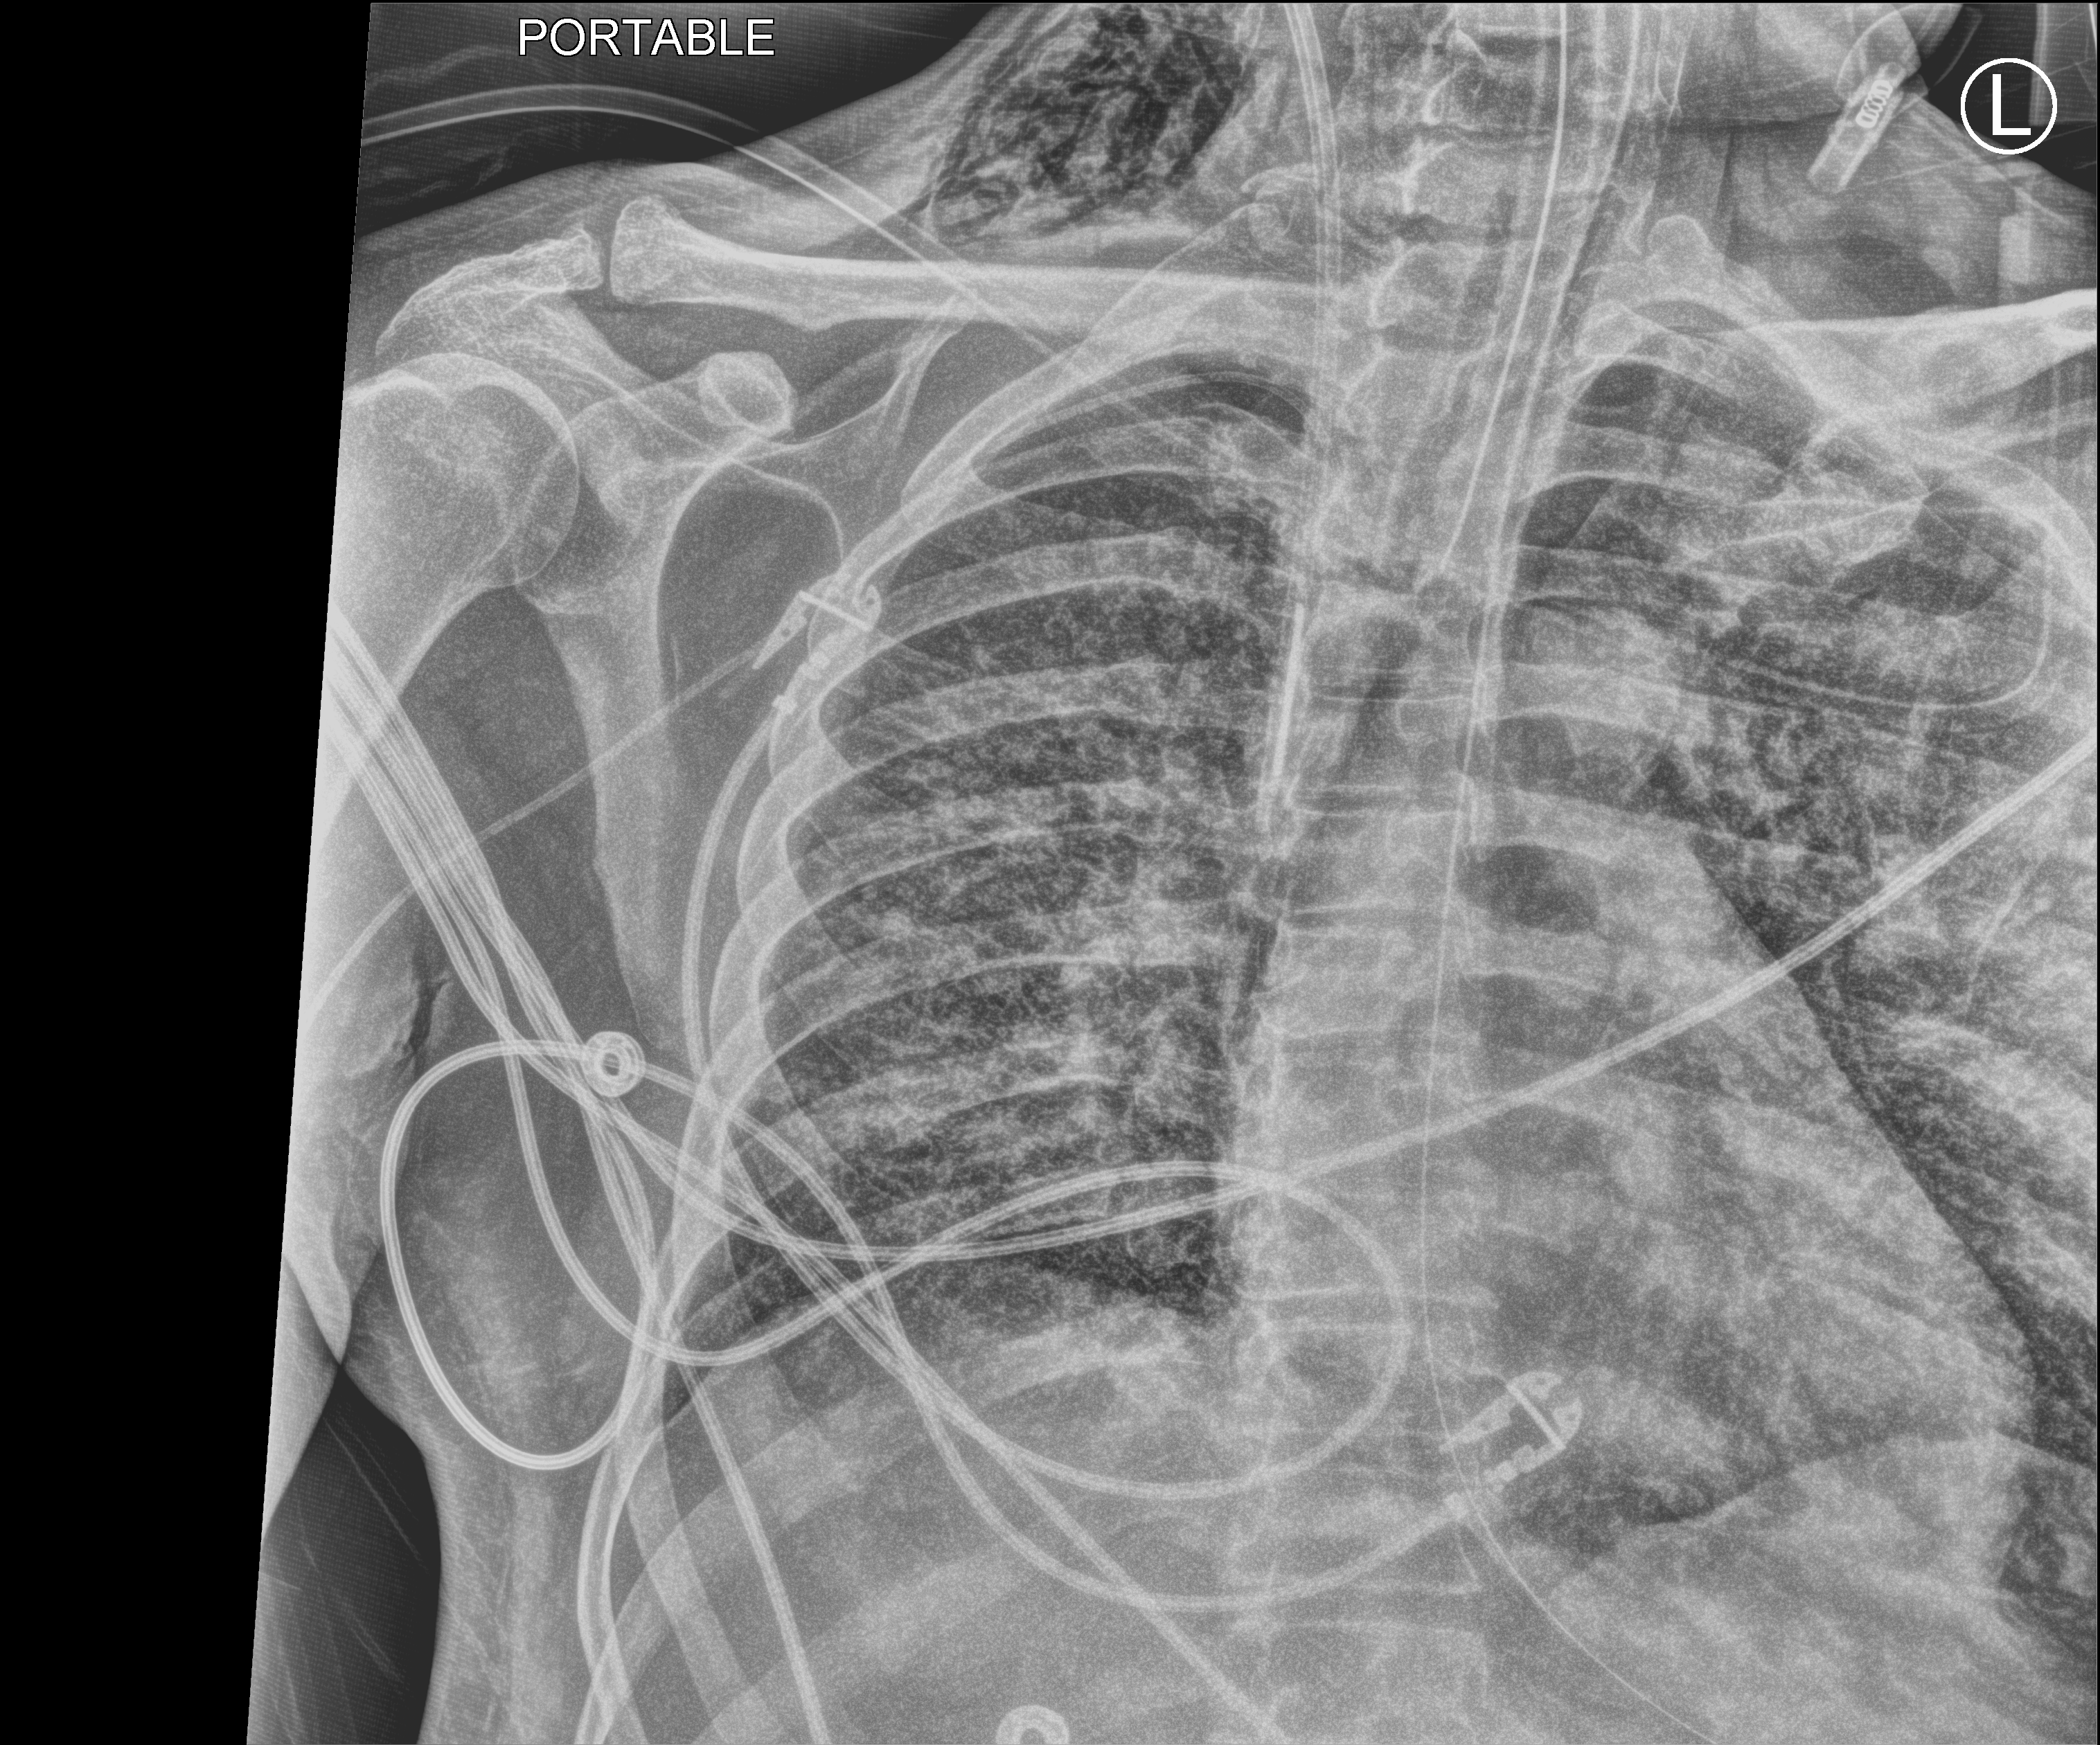
Bedside chest radiograph (computed radiography). Patient hospitalised with COVID-19; male, aged 18–59 years.
Admission-level facts for this patient (not findings on this image; timing relative to this image not recorded): COPD (admission record): no; admitted to intensive care during this hospital stay: yes; mechanically ventilated during this hospital stay: yes.